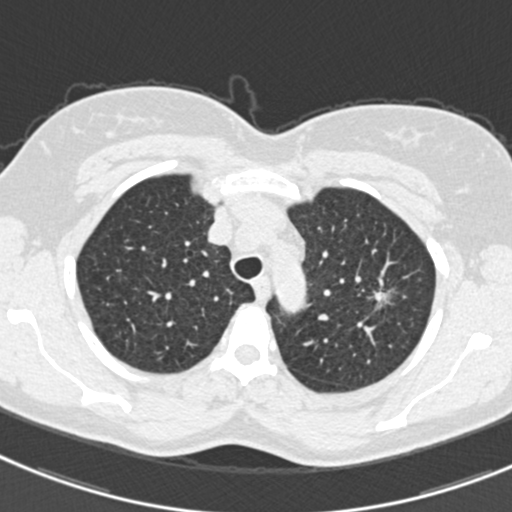
Low-dose screening chest CT, one axial slice; slice 248 of 309 in the series (ordered by position); 120 kVp; lung window (W 1500 / L -600 HU); 512 × 512 image matrix, field of view 302 × 302 mm.
Outlined on this slice (manually delineated by an expert):
- lesion 1 (tumor, upper lobe of left lung): box from (x=374, y=292) to (x=389, y=304) px